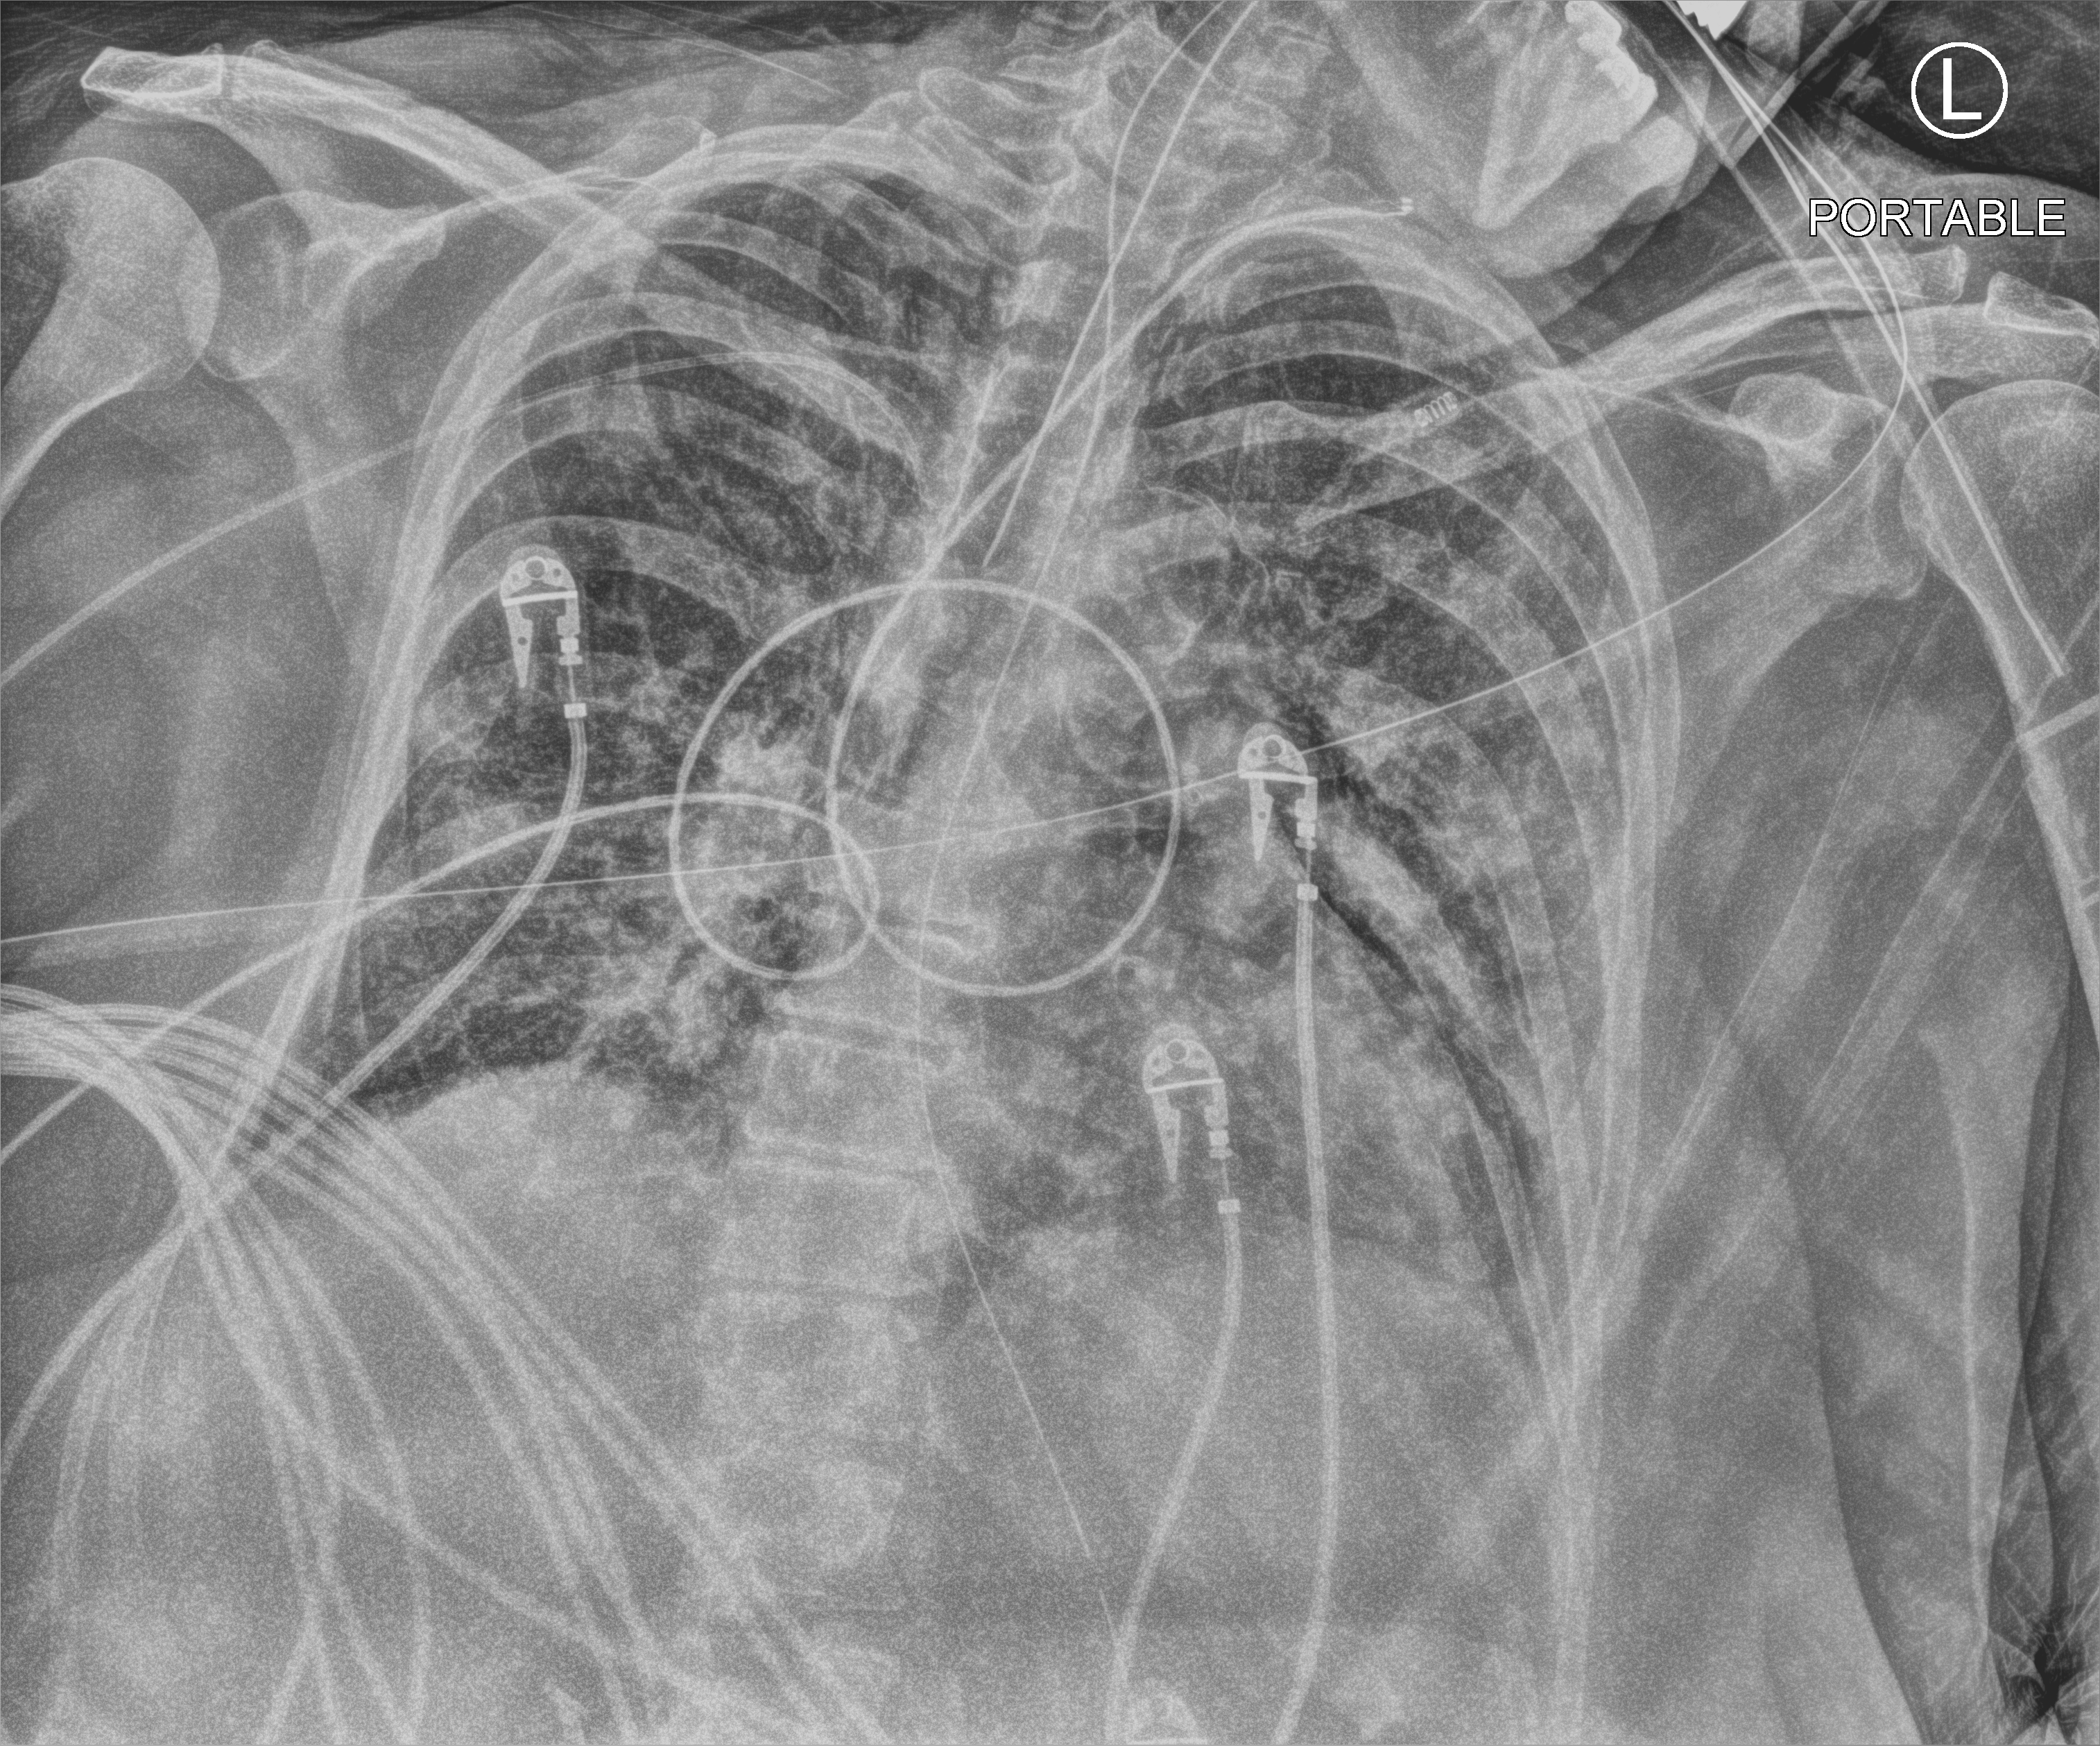
Bedside chest radiograph (computed radiography), anteroposterior (AP) projection. Patient hospitalised with COVID-19; female, aged 60–74 years.
Hospital-stay facts (about this admission, not read from this image; timing relative to this image not recorded): admitted to intensive care during this hospital stay: yes; hypertension (admission record): yes.